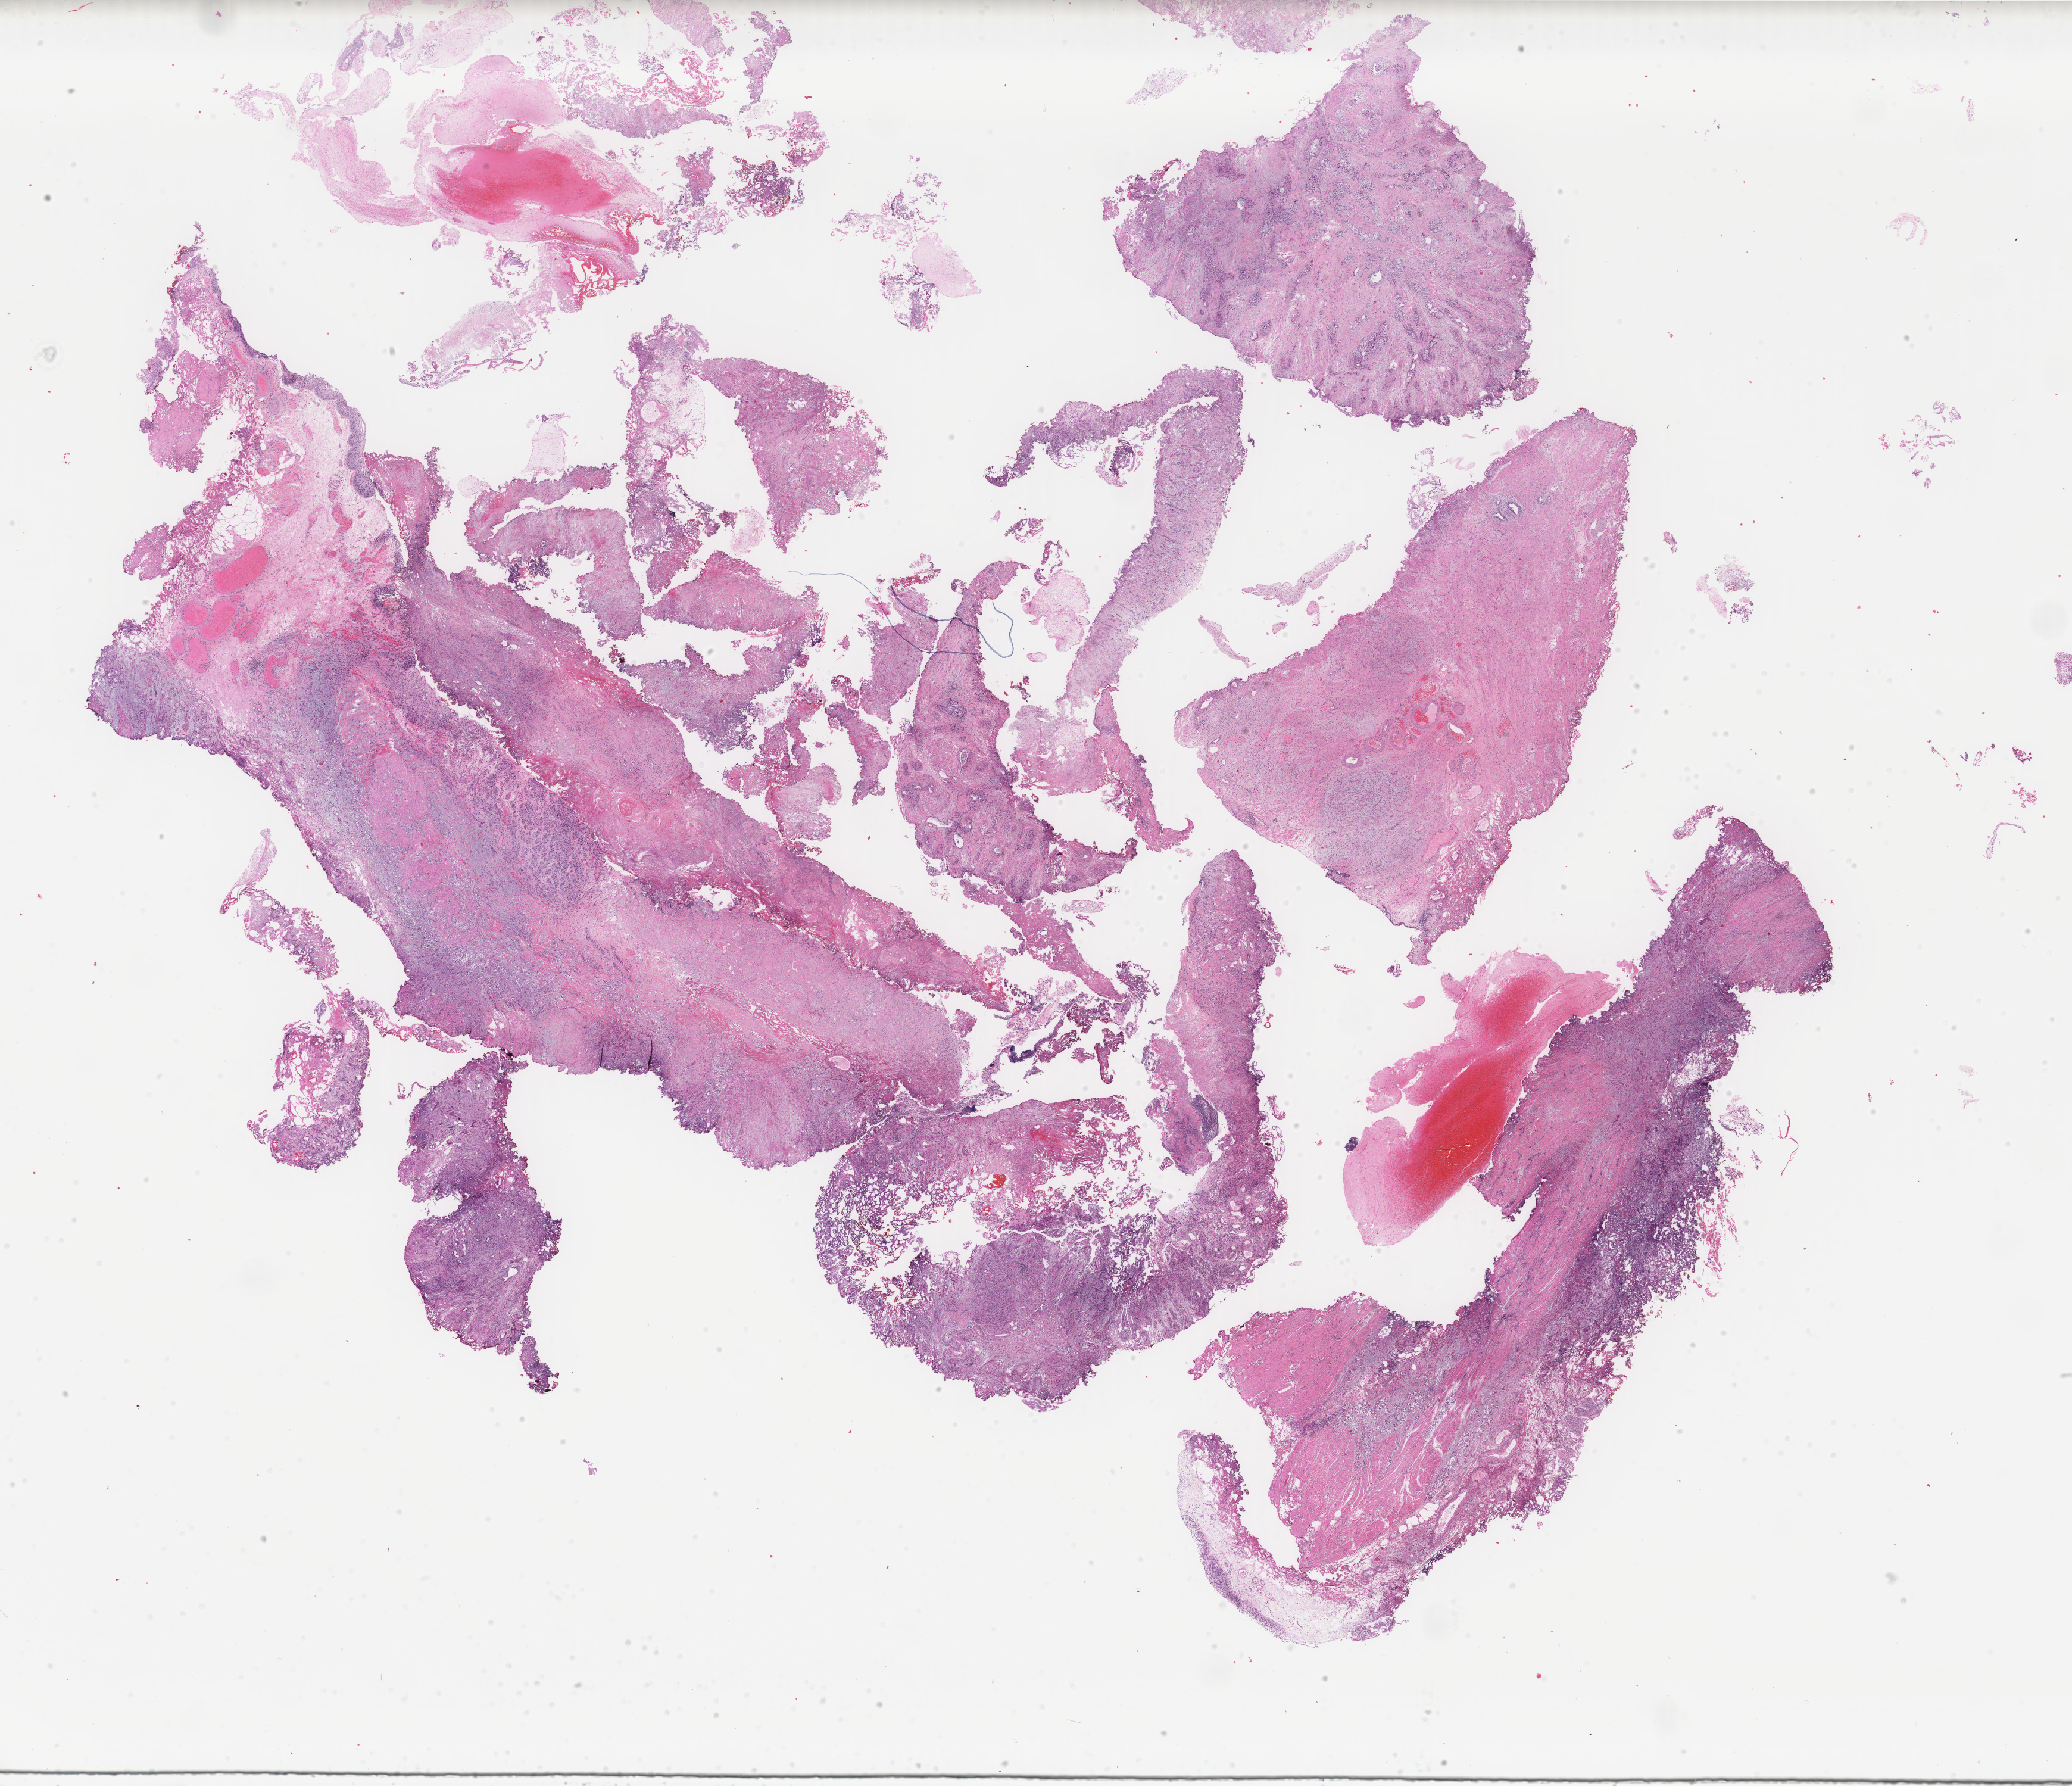
Digitized H&E tissue section (whole slide) — a low-resolution overview of the entire scanned area, about 27.6 x 23.8 mm; FFPE section; sample: primary tumour, bladder. Patient: male, age at initial diagnosis 57 years.
Diagnosis: Transitional cell carcinoma.